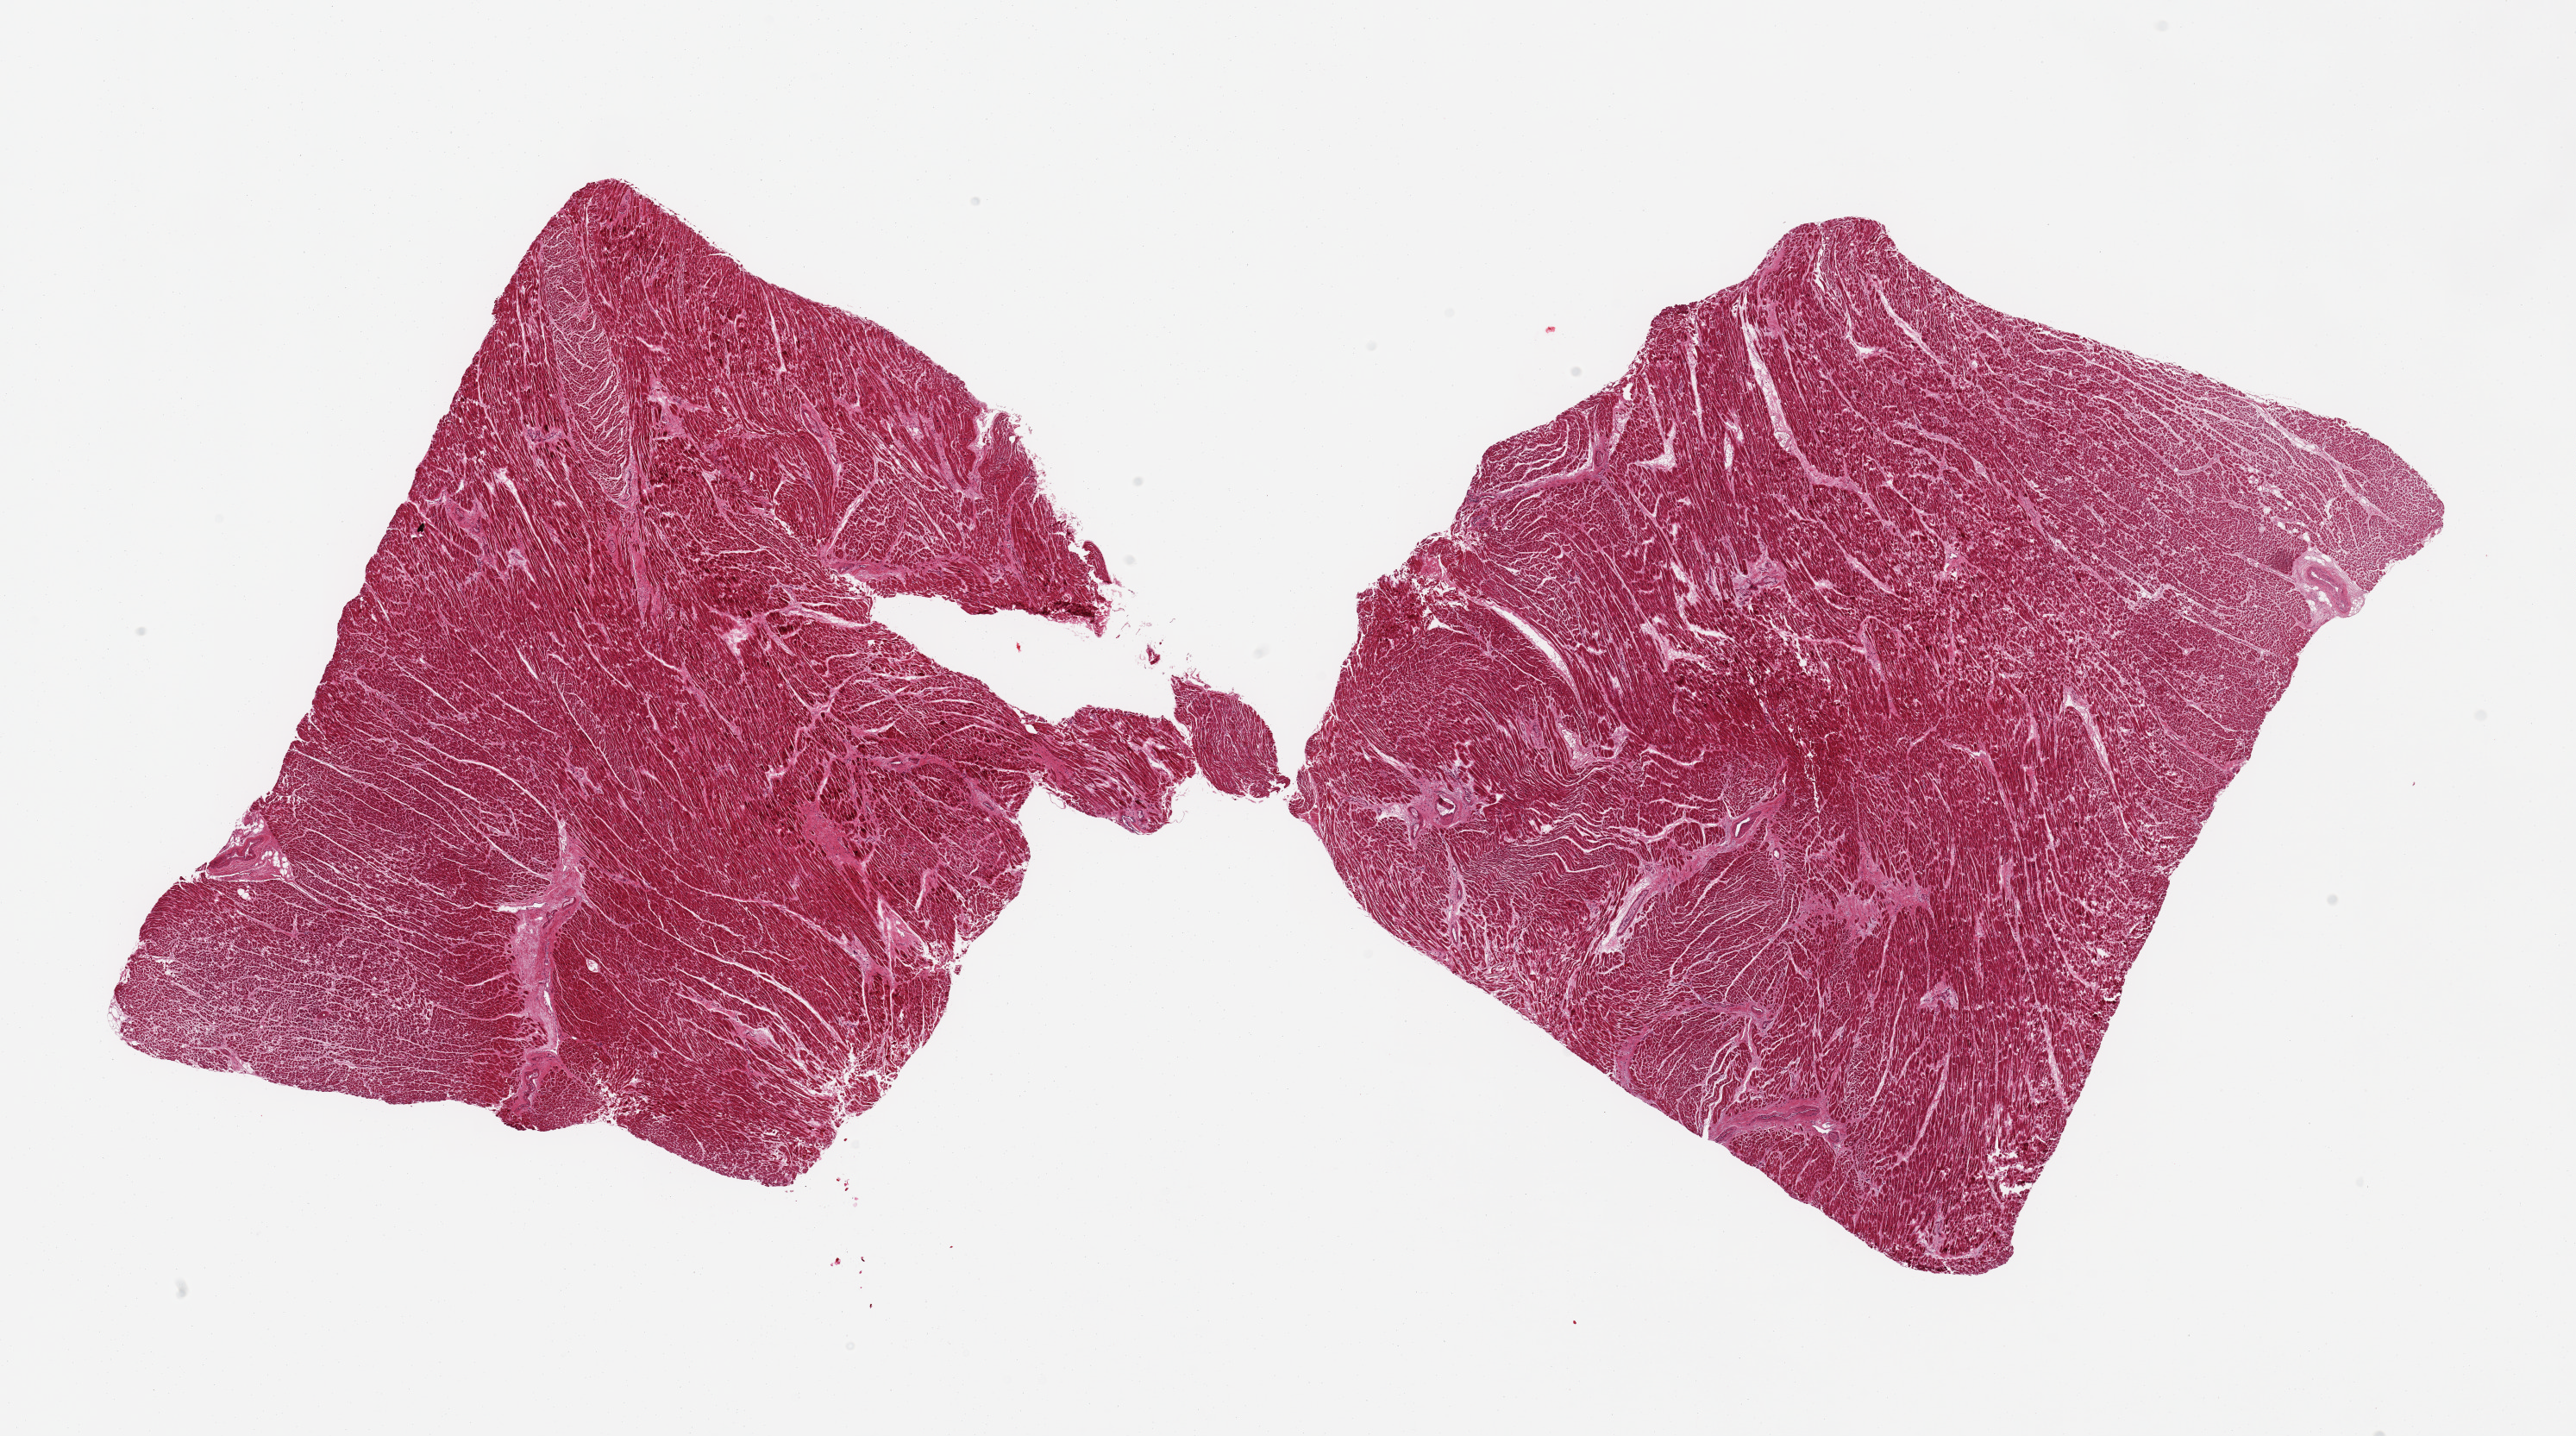
Digitized hematoxylin and eosin (H&E)-stained section — low-resolution overview of the scanned area, about 23.6 x 13.2 mm (acquisition: 20x scan); PAXgene-fixed, paraffin-embedded tissue; target tissue: heart; tissue donor sample. Donor: female.
Review note (as recorded): 2 pieces; diffuse interstitial fibrosis with scarring, patchy eosinophilia (? recent ischemia).